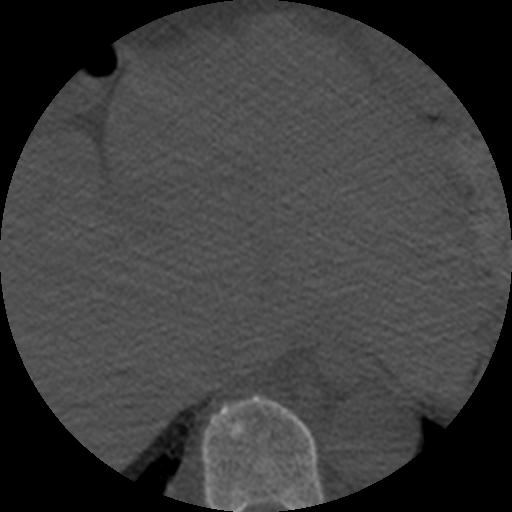
CT including the spine, one axial slice; slice 286 of 508 in the series (ordered by position); 120 kVp; bone window (W 1800 / L 400 HU); 512 × 512 image matrix, field of view 160 × 160 mm. Patient age 57 years. From the clinical record (not read from this slice): primary cancer: prostate.
Structures marked on this image (semi-automatic segmentation, software-assisted and operator-edited):
- T9 vertebra: bounding box <201,394,324,512> (left, top, right, bottom; pixels)